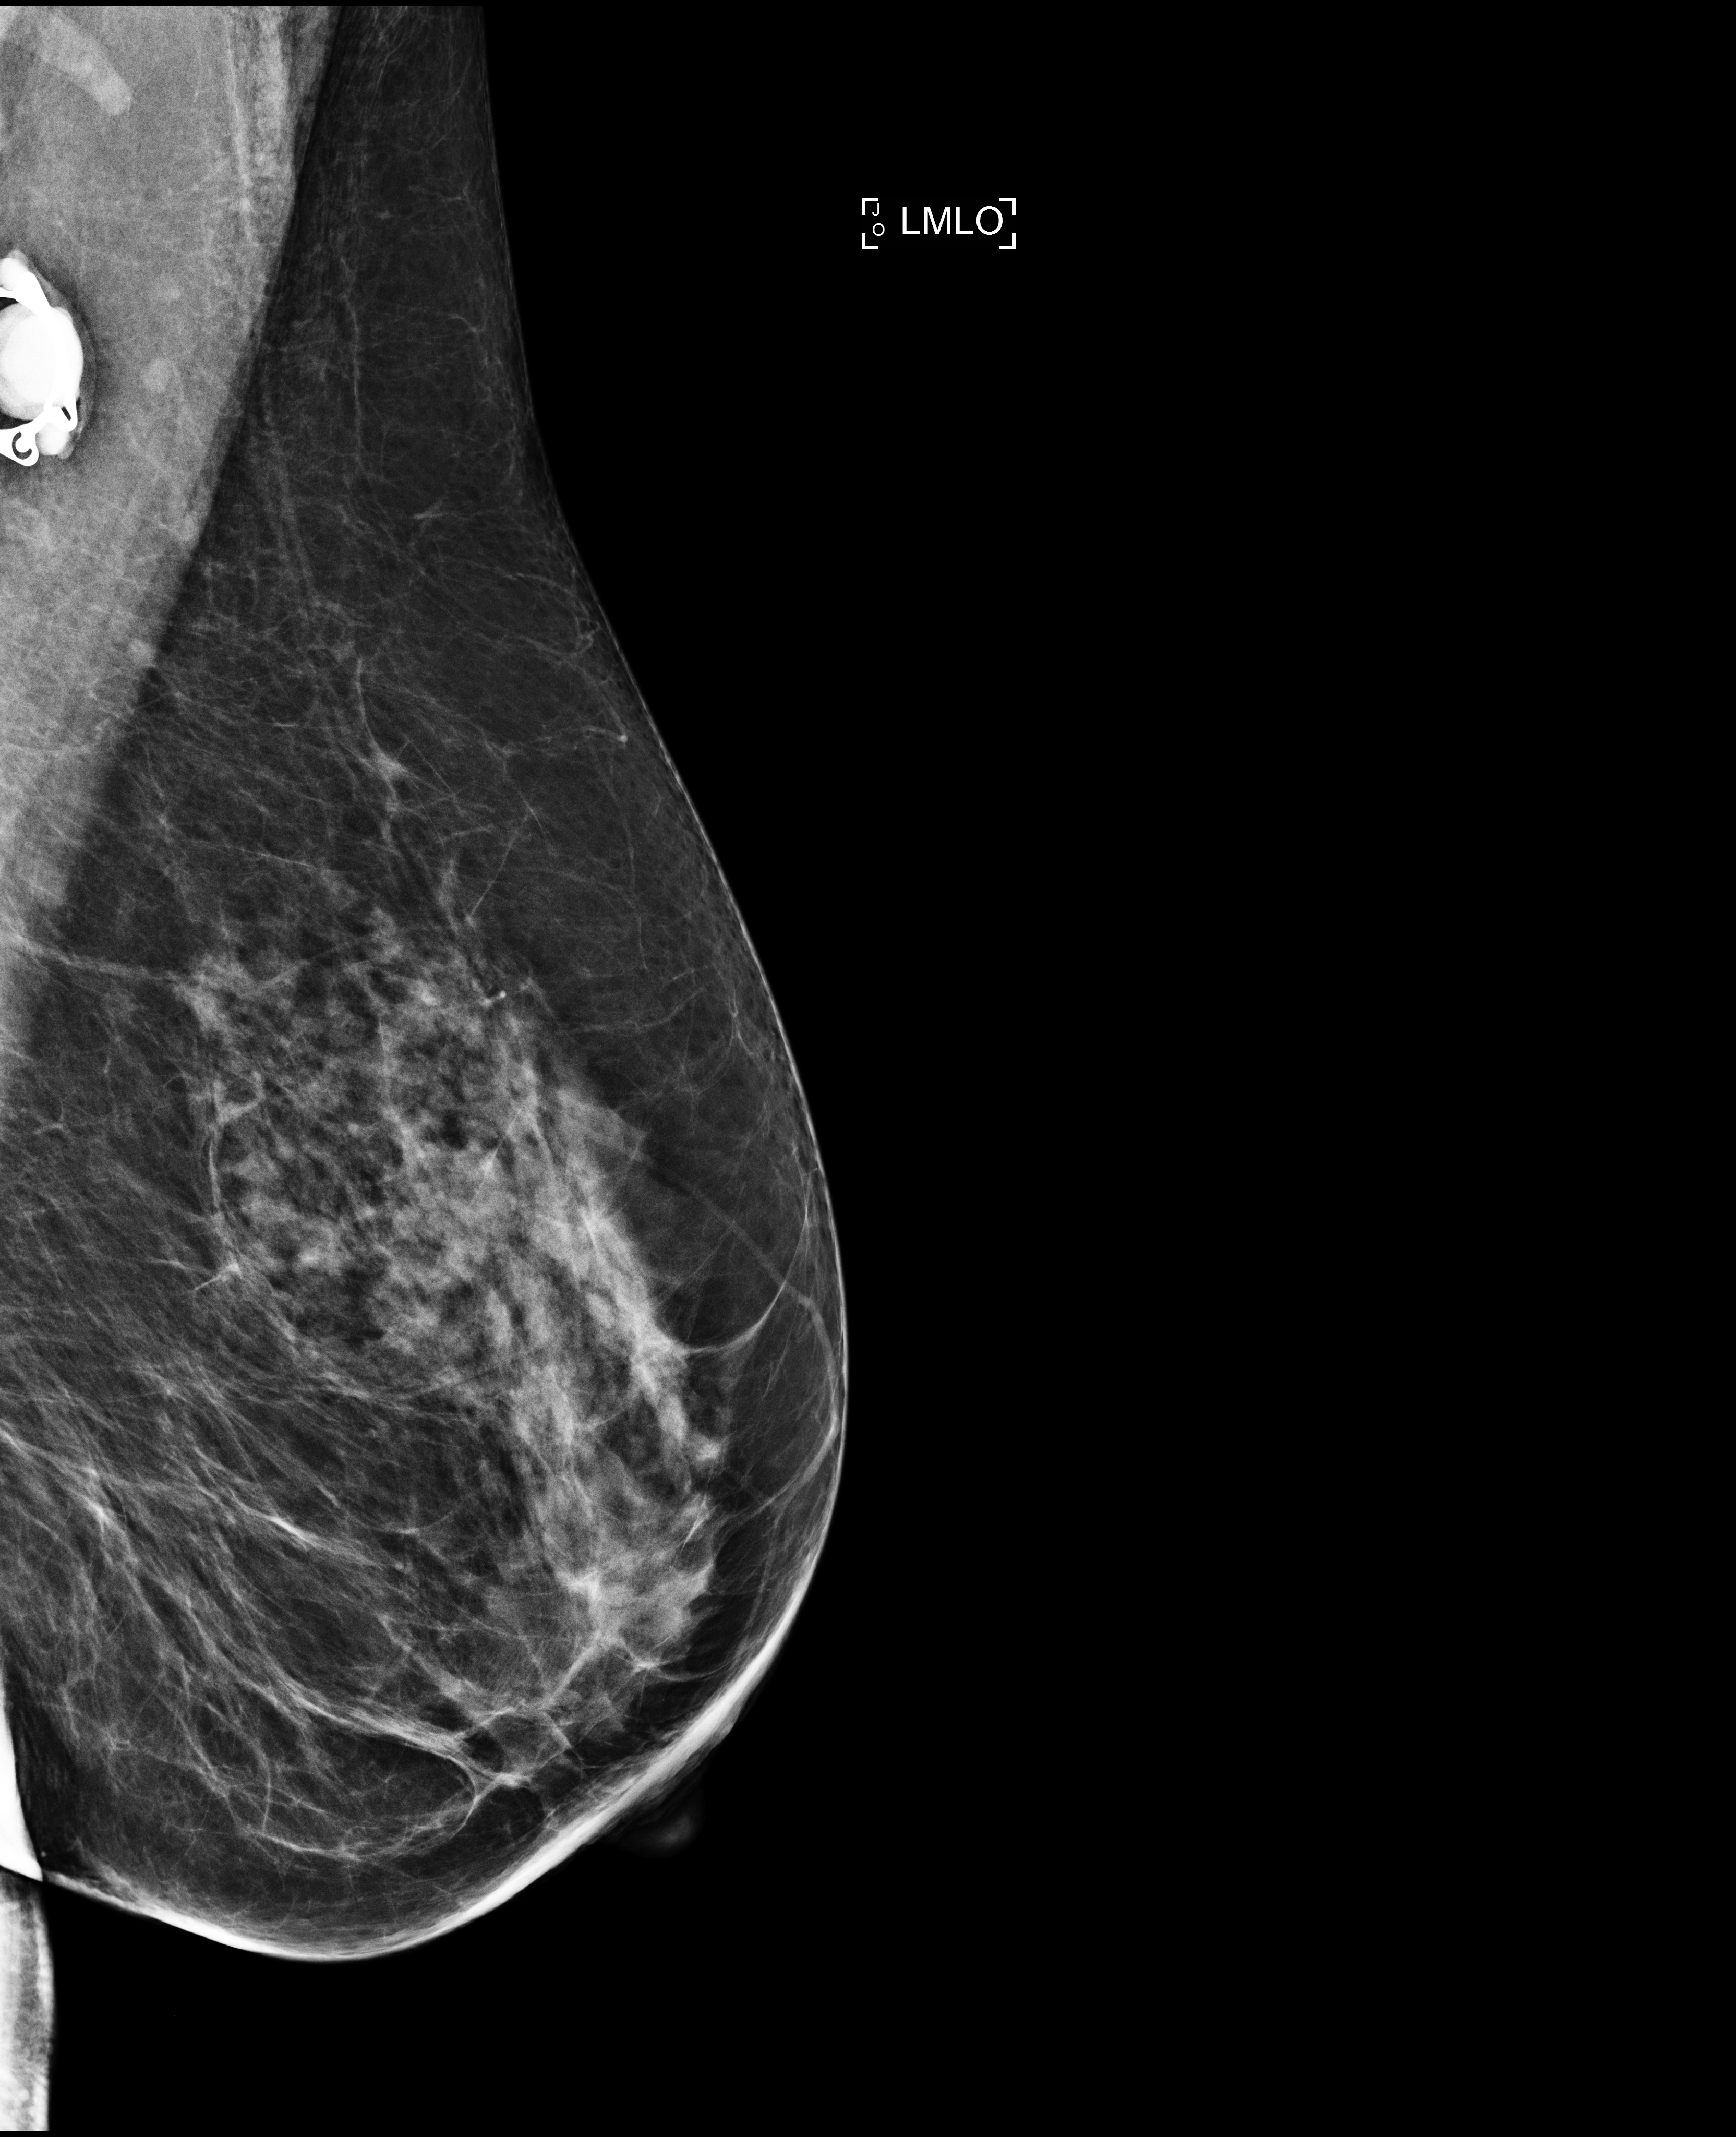
Digital mammogram (FFDM), left breast, mediolateral oblique (MLO) view, screening examination, compressed breast thickness 68 mm, system: Selenia Dimensions. Patient: female, 57 years.
Breast density at the screening exam (both breasts): heterogeneously dense (BI-RADS density category c). Final BI-RADS assessment for this screening round (tomosynthesis exam, both breasts): category 1. Recall: no recall after this screen.